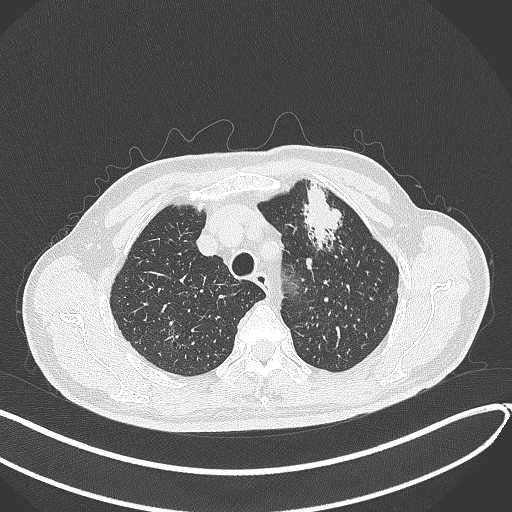
Chest CT, one axial slice. Position 342 of 459 along the scan axis. 120 kVp. Lung window (W 1500 / L -600 HU). 1 mm slice thickness. 512 × 512 image matrix. Male patient, age 74 years. Case-level facts recorded for this patient, not image findings: clinical TNM (as recorded): T2b N0 M1c.
Outlined on this slice (rectangle marked by the reading radiologist):
- lung tumour (recorded histology: adenocarcinoma): bounding box (x1, y1, x2, y2) in pixels: (298, 182, 349, 253)